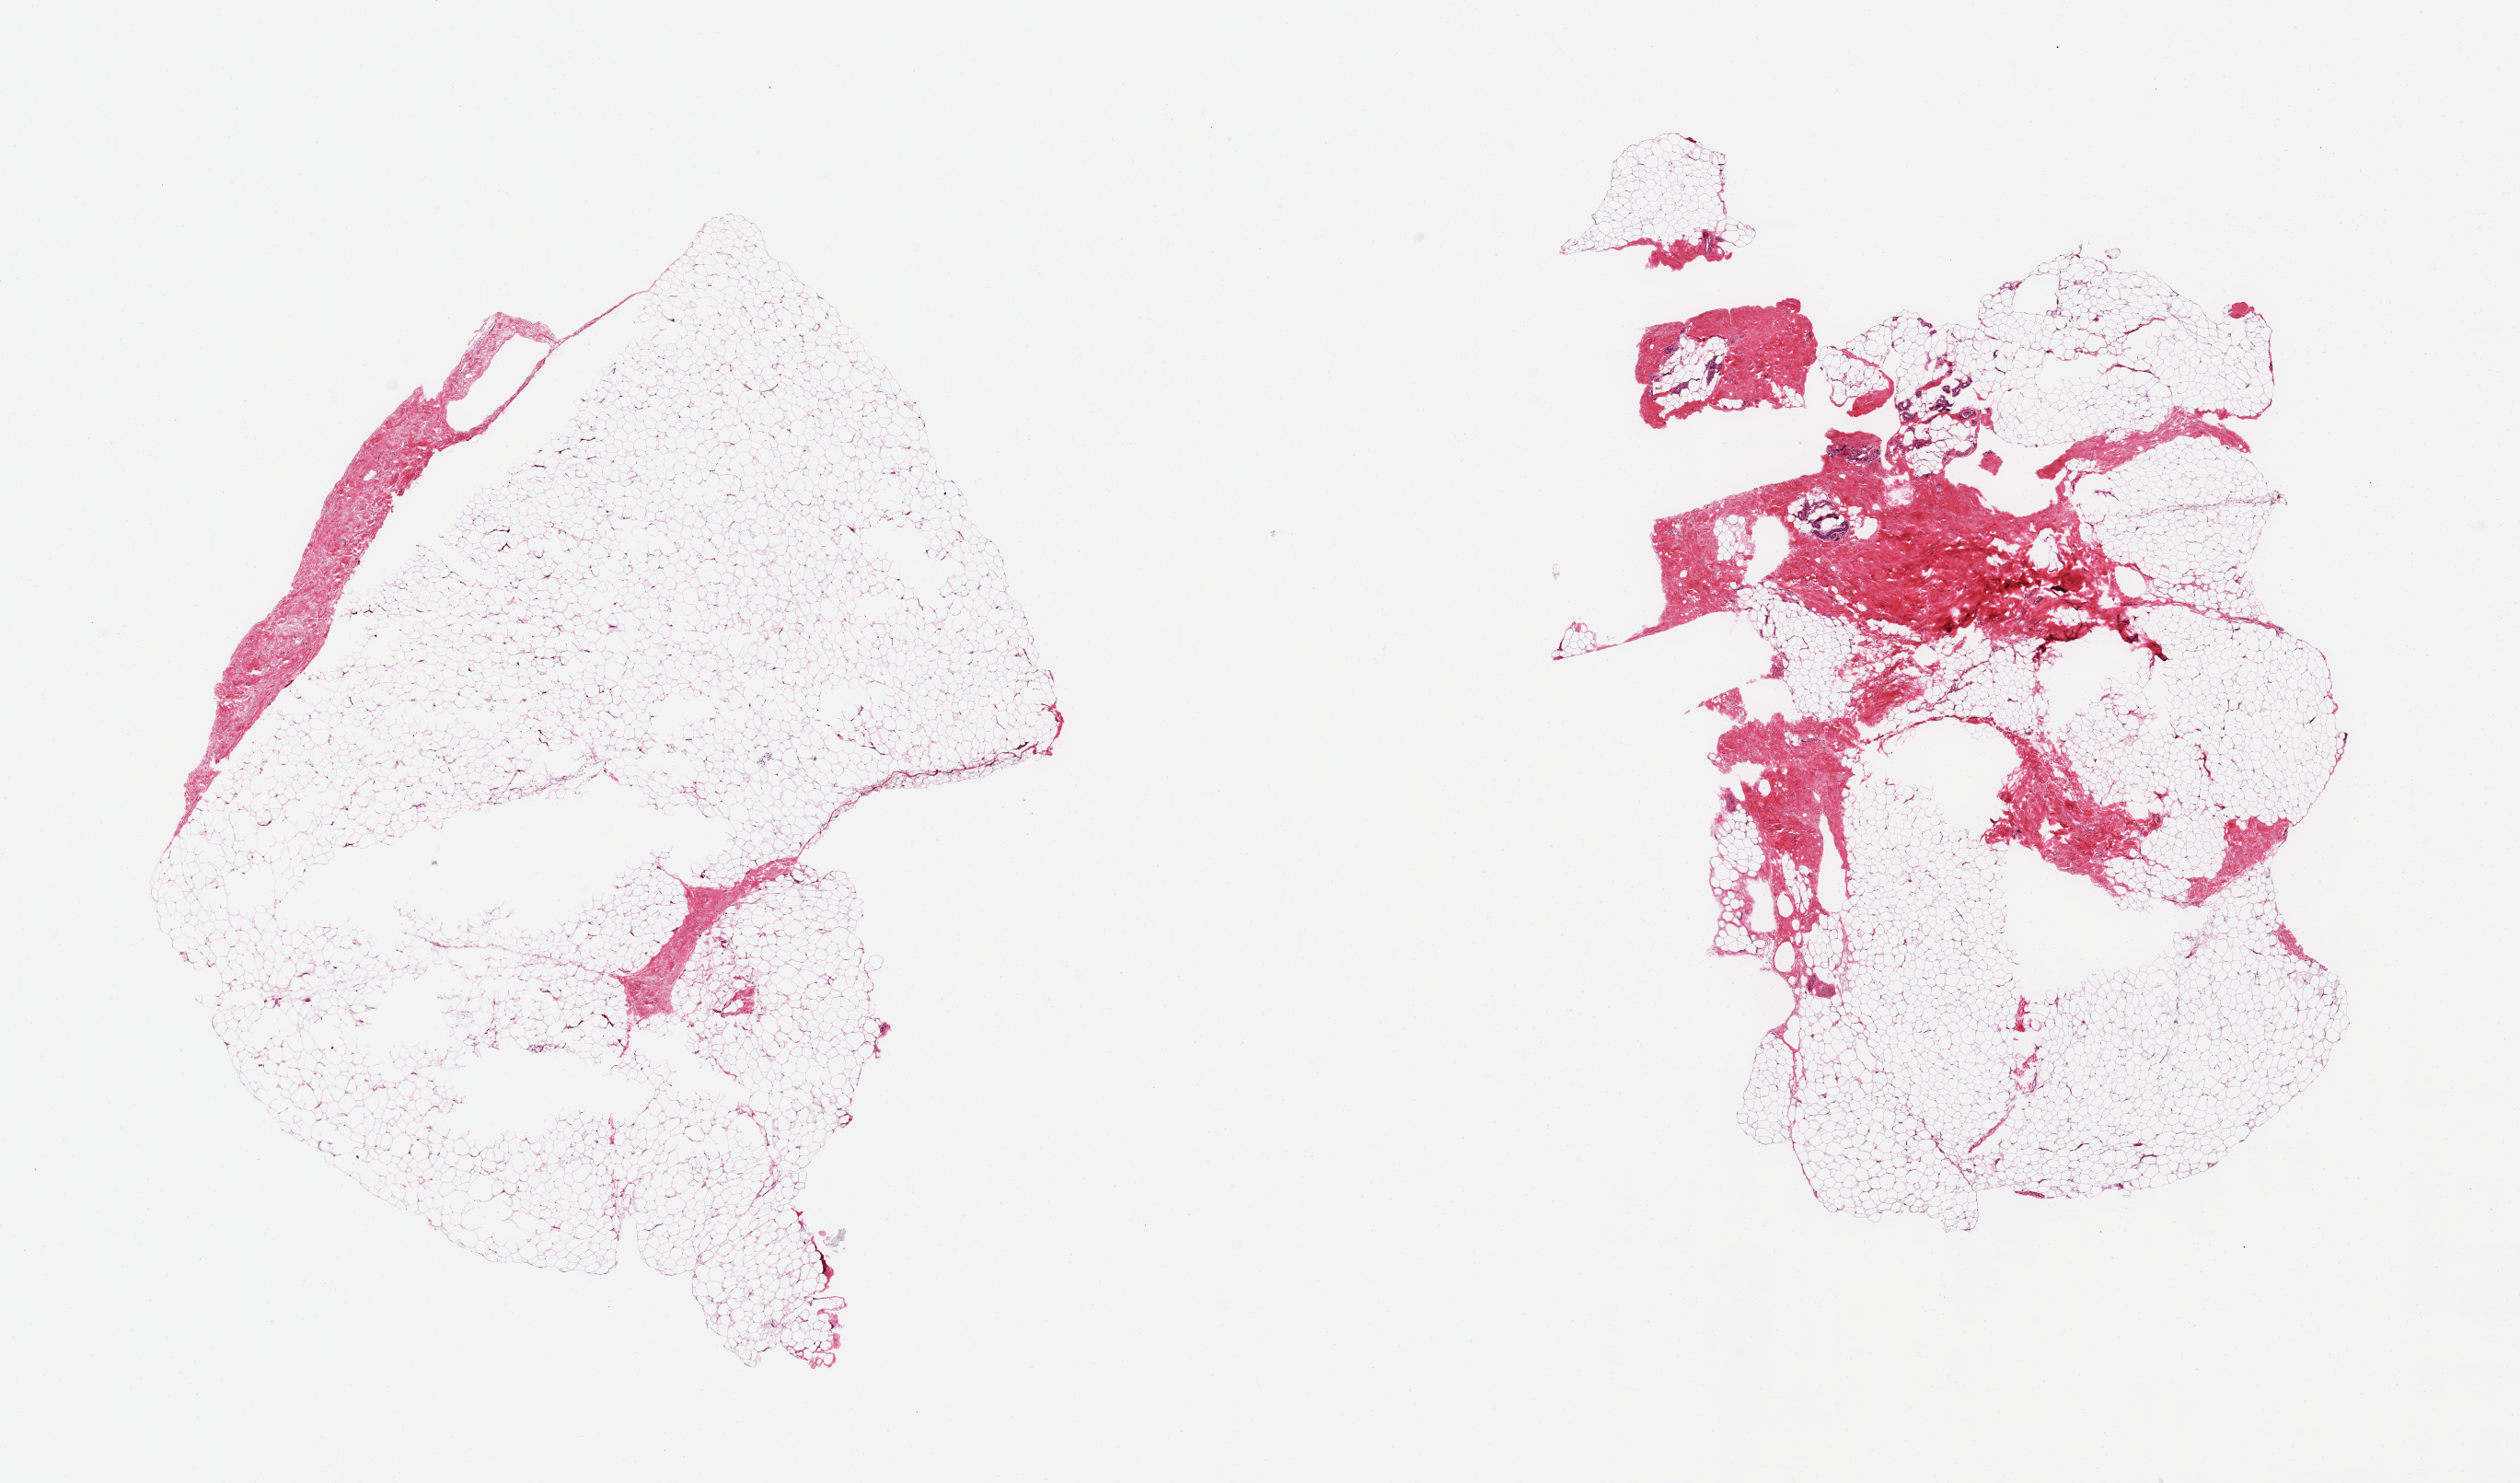
Digitized hematoxylin and eosin (H&E)-stained section — a low-resolution overview of the entire scanned area, about 21.7 x 12.7 mm. Donor: female.
Specimen: PAXgene-fixed, paraffin-embedded tissue; section of adipose tissue (target tissue); donor tissue sample.